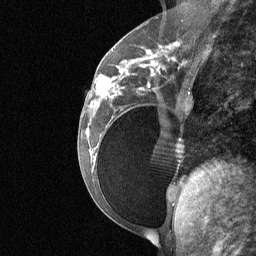
Breast MRI (dynamic contrast-enhanced), one sagittal slice. Slice 27 of 64 in the series (ordered by position). Dynamic contrast-enhanced study with each time point stored as its own series, time point 2 of 3 at this slice position (early post-contrast, ordered by acquisition time). 1.5 T. TE 4.8 ms, TR 27 ms. 256 × 256 image matrix, field of view 200 × 200 mm. Patient: female, 34 years. From the clinical record (not read from this slice): setting: breast cancer imaged before/during neoadjuvant chemotherapy; receptor status: HR-positive, HER2-negative.
Outlined on this slice (semi-automatically segmented with operator editing):
- analysis volume of interest (the breast-tissue region the enhancement analysis was run in; not a lesion): bounding box <92,50,188,185> (left, top, right, bottom; pixels)
- tumour enhancement mask (voxels above the 90 % enhancement threshold inside the analysis volume of interest): <97,56,154,98>